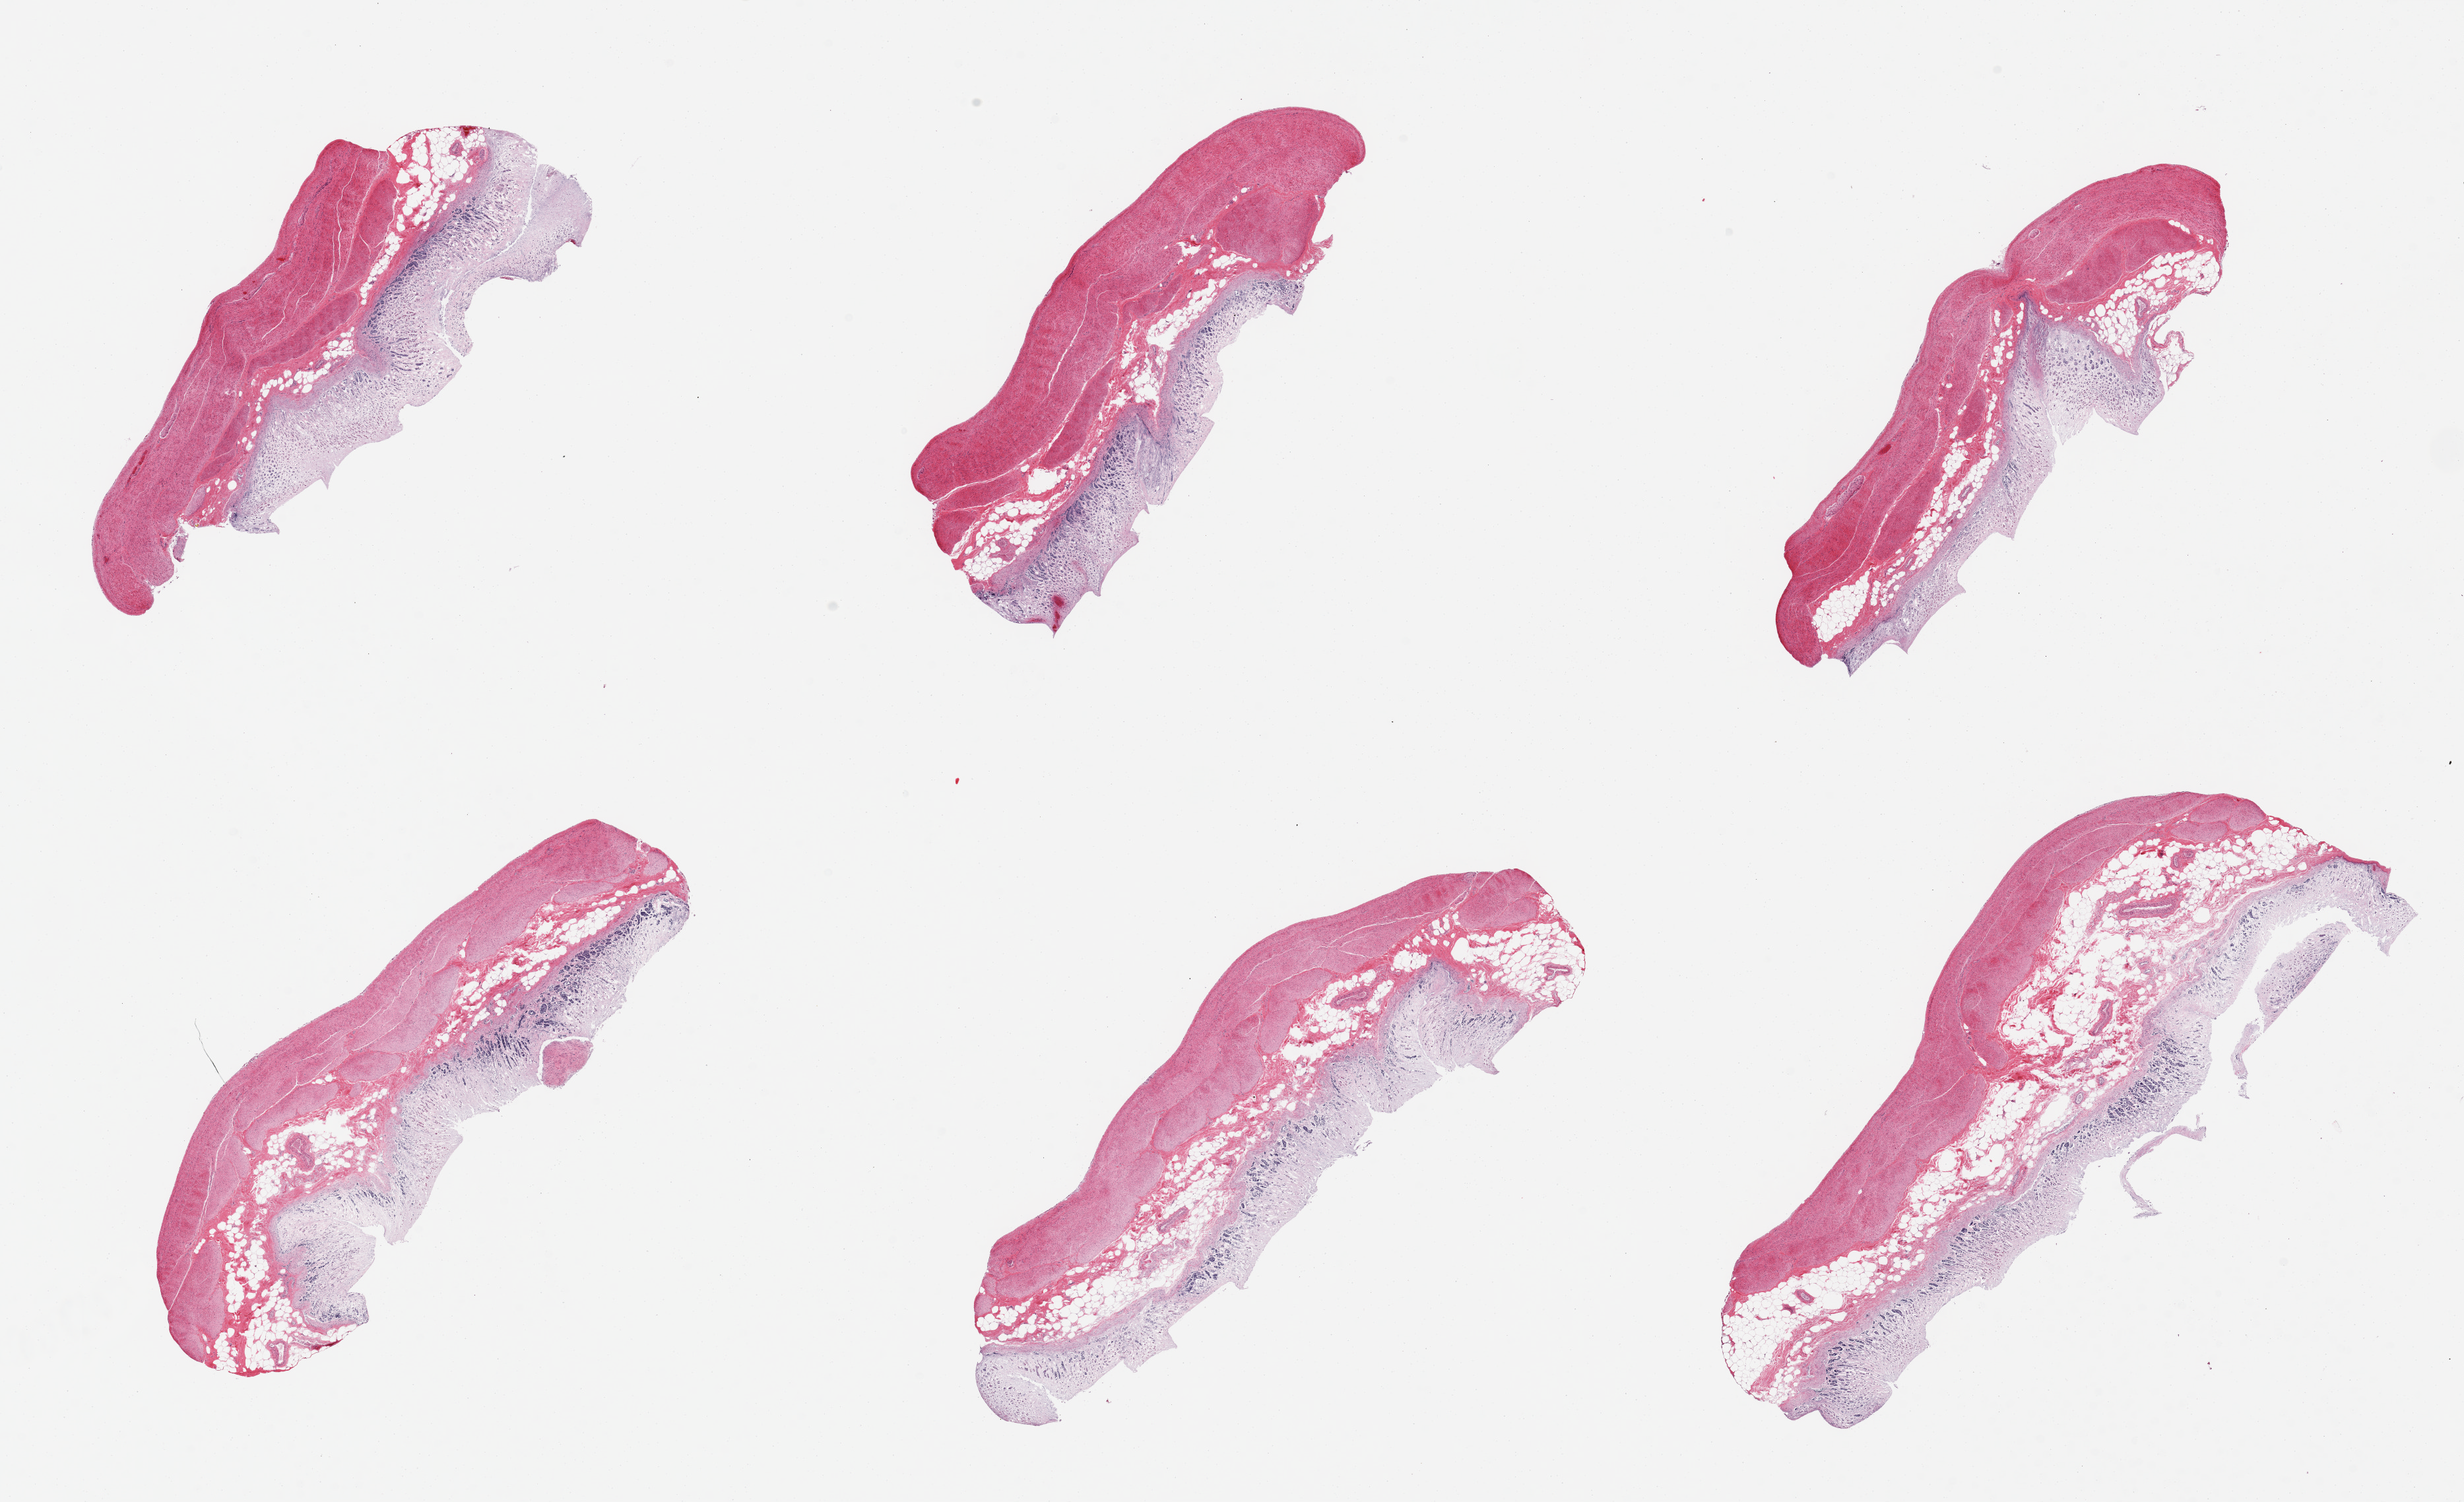
Digitized H&E-stained section, brightfield, a low-resolution overview of the entire scanned area, about 29.5 x 18.0 mm (from a 20x scan), PAXgene-fixed, paraffin-embedded tissue, target tissue: stomach, donor tissue sample. Male donor.
Reviewer comment on this tissue sample: 6 pieces, mucosa is ~~1mm thick, ~50%, but totally autolyzed.